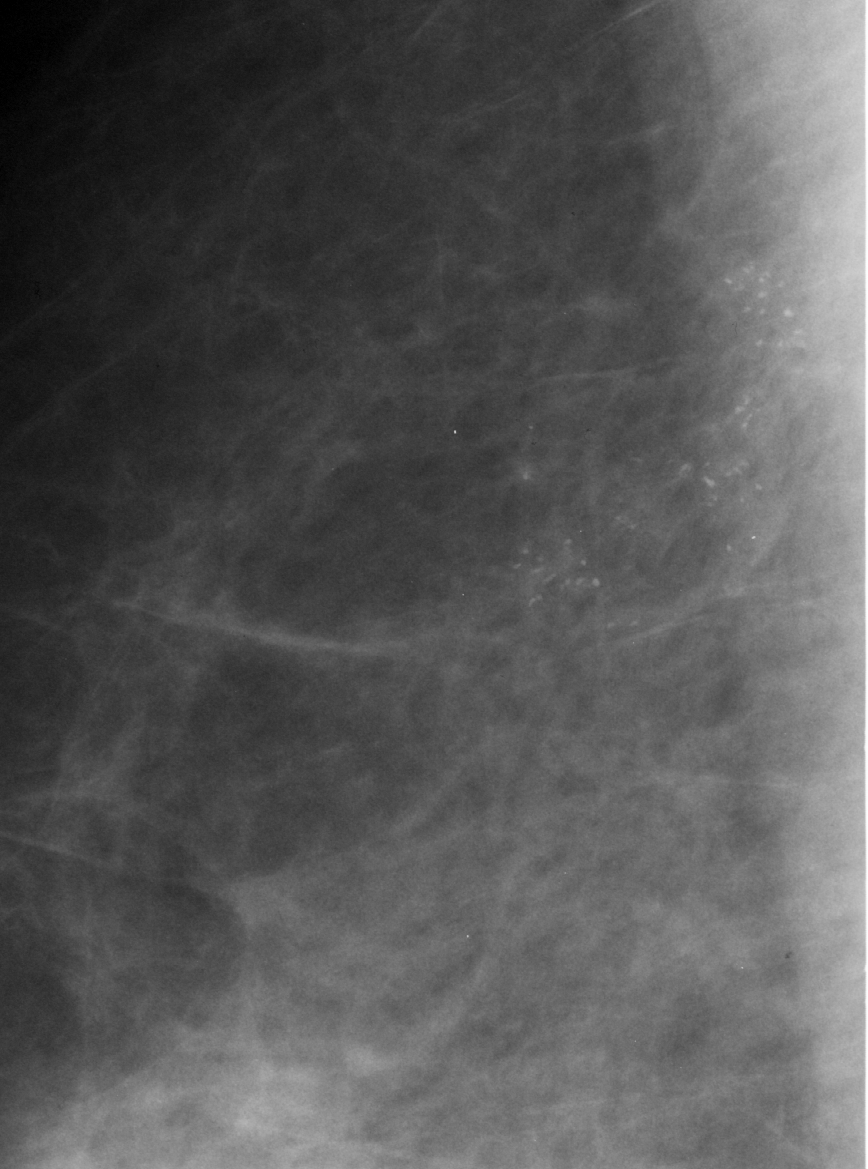
Region of interest cut from a scanned film mammogram (one marked finding), right breast, MLO view, BI-RADS breast density category 3 (scale 1–4).
Calcifications, morphology pleomorphic, distribution segmental; BI-RADS assessment category 5; pathology result (as recorded, not read from the image): malignant.